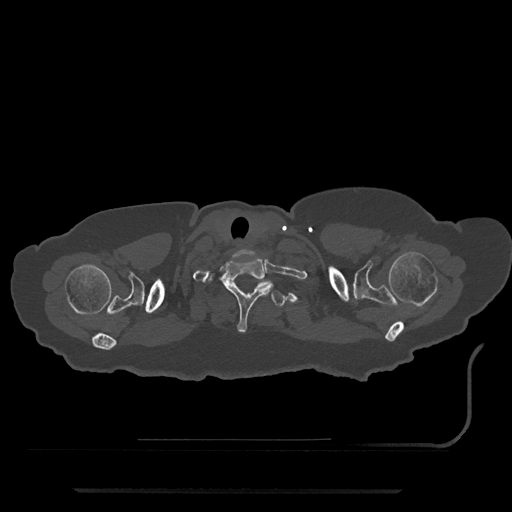
CT including the spine, one axial slice. Position 705 of 797 along the scan axis. Reconstruction kernel Br40s/3. Bone window (W 1800 / L 400 HU). 0.5 mm slice thickness. 512 × 512 image matrix, field of view 440 × 440 mm. Patient: female, 51 years. From the clinical record (not read from this slice): primary cancer: neuro; vertebrae with lytic lesions (as recorded): T8.
Outlined on this slice (semi-automatic segmentation, software-assisted and operator-edited):
- T1 vertebra: bounding box [x1, y1, x2, y2] px = [210, 258, 293, 333]
- T2 vertebra: [256, 280, 285, 307]